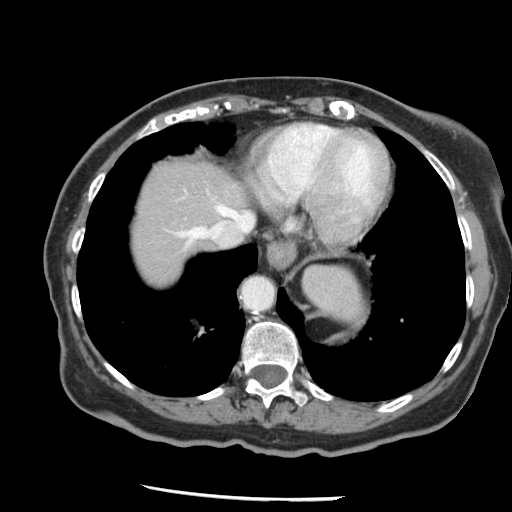
Contrast-enhanced abdominal CT, one axial slice; position 117 of 148 along the scan axis; reconstruction kernel STANDARD; soft-tissue window (W 400 / L 40 HU); 512 × 512 image matrix, field of view 330 × 330 mm. Female patient, age 85 years. From the clinical record (not read from this slice): diagnosis: colorectal cancer liver metastases, imaged before liver resection; multiple liver metastases: no; largest metastasis: 0.9 cm; disease in both lobes: no.
Outlined on this slice (expert manual segmentation):
- hepatic veins: box from (x=179, y=205) to (x=254, y=246) px
- liver: (x=128, y=161)–(x=256, y=289)
- planned liver remnant (the part of the liver to remain after resection): (x=128, y=161)–(x=256, y=289)